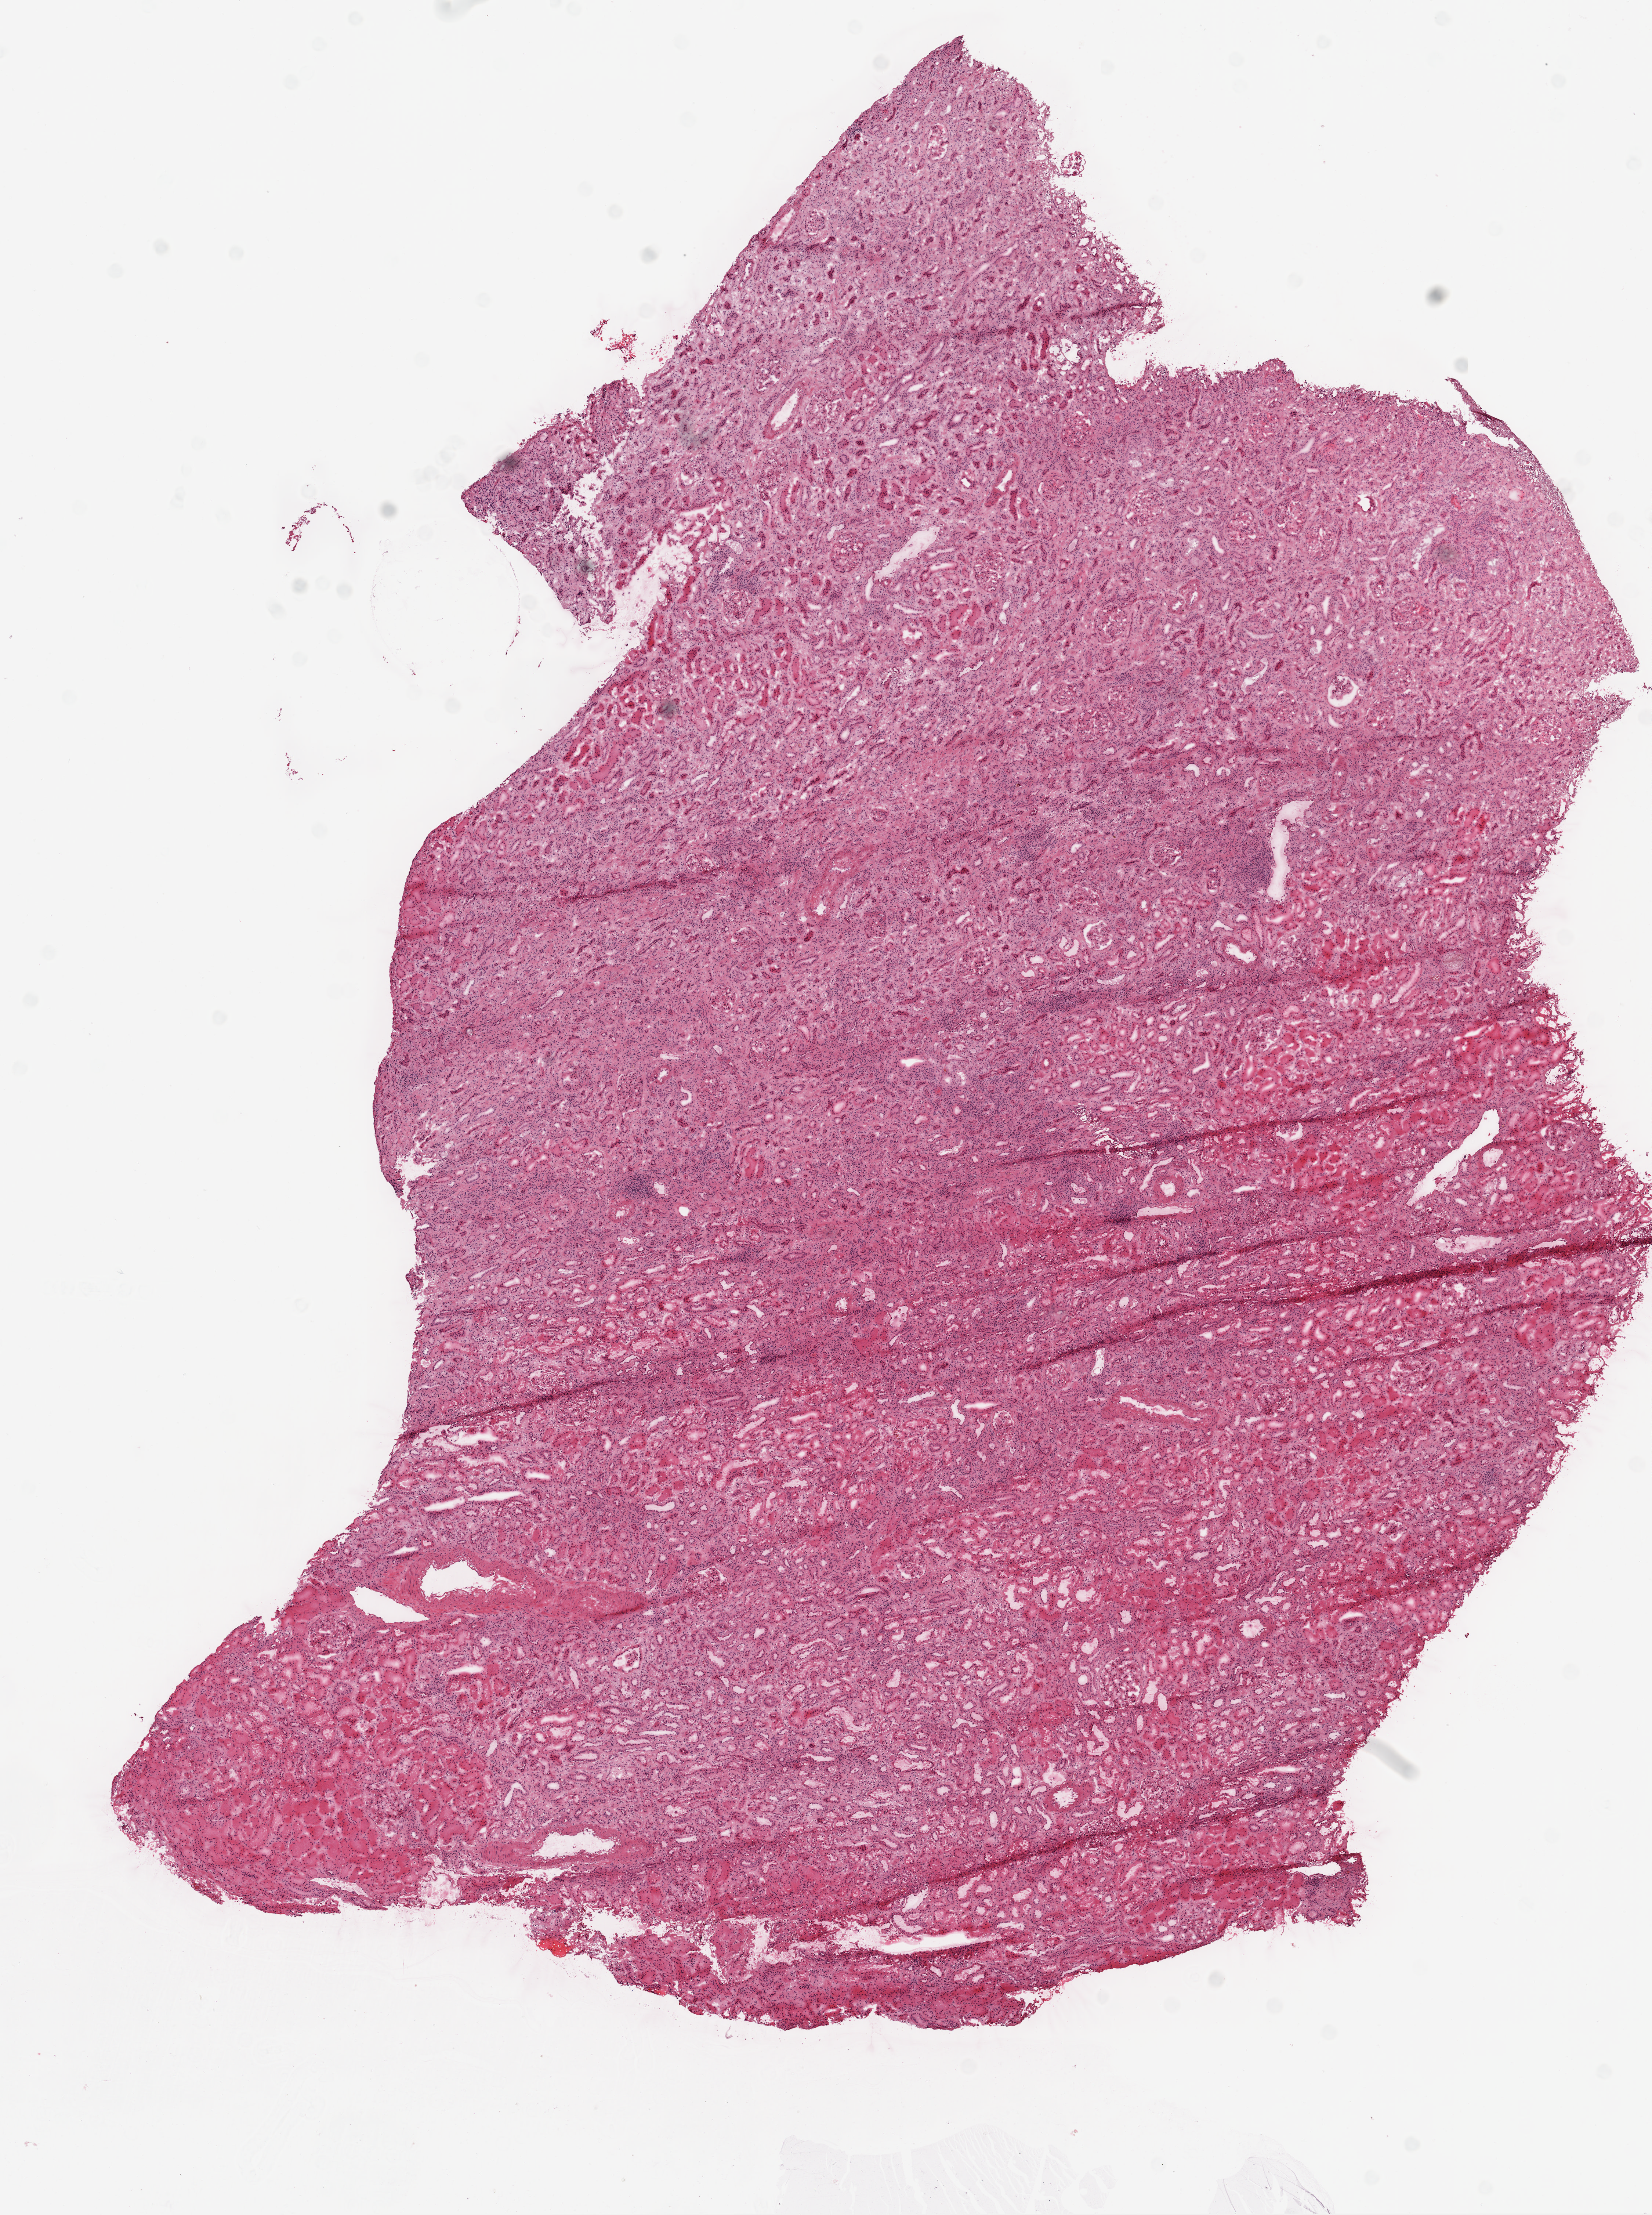
Whole-slide histology image, H&E, whole scanned area (about 9.0 x 12.1 mm) shown as a low-resolution overview, frozen section, sample: solid tissue normal (non-tumour tissue), kidney. Male patient; age at initial diagnosis 42 years.
This section: solid tissue normal sample (biorepository sample class). Patient diagnosis: Clear cell adenocarcinoma, NOS.